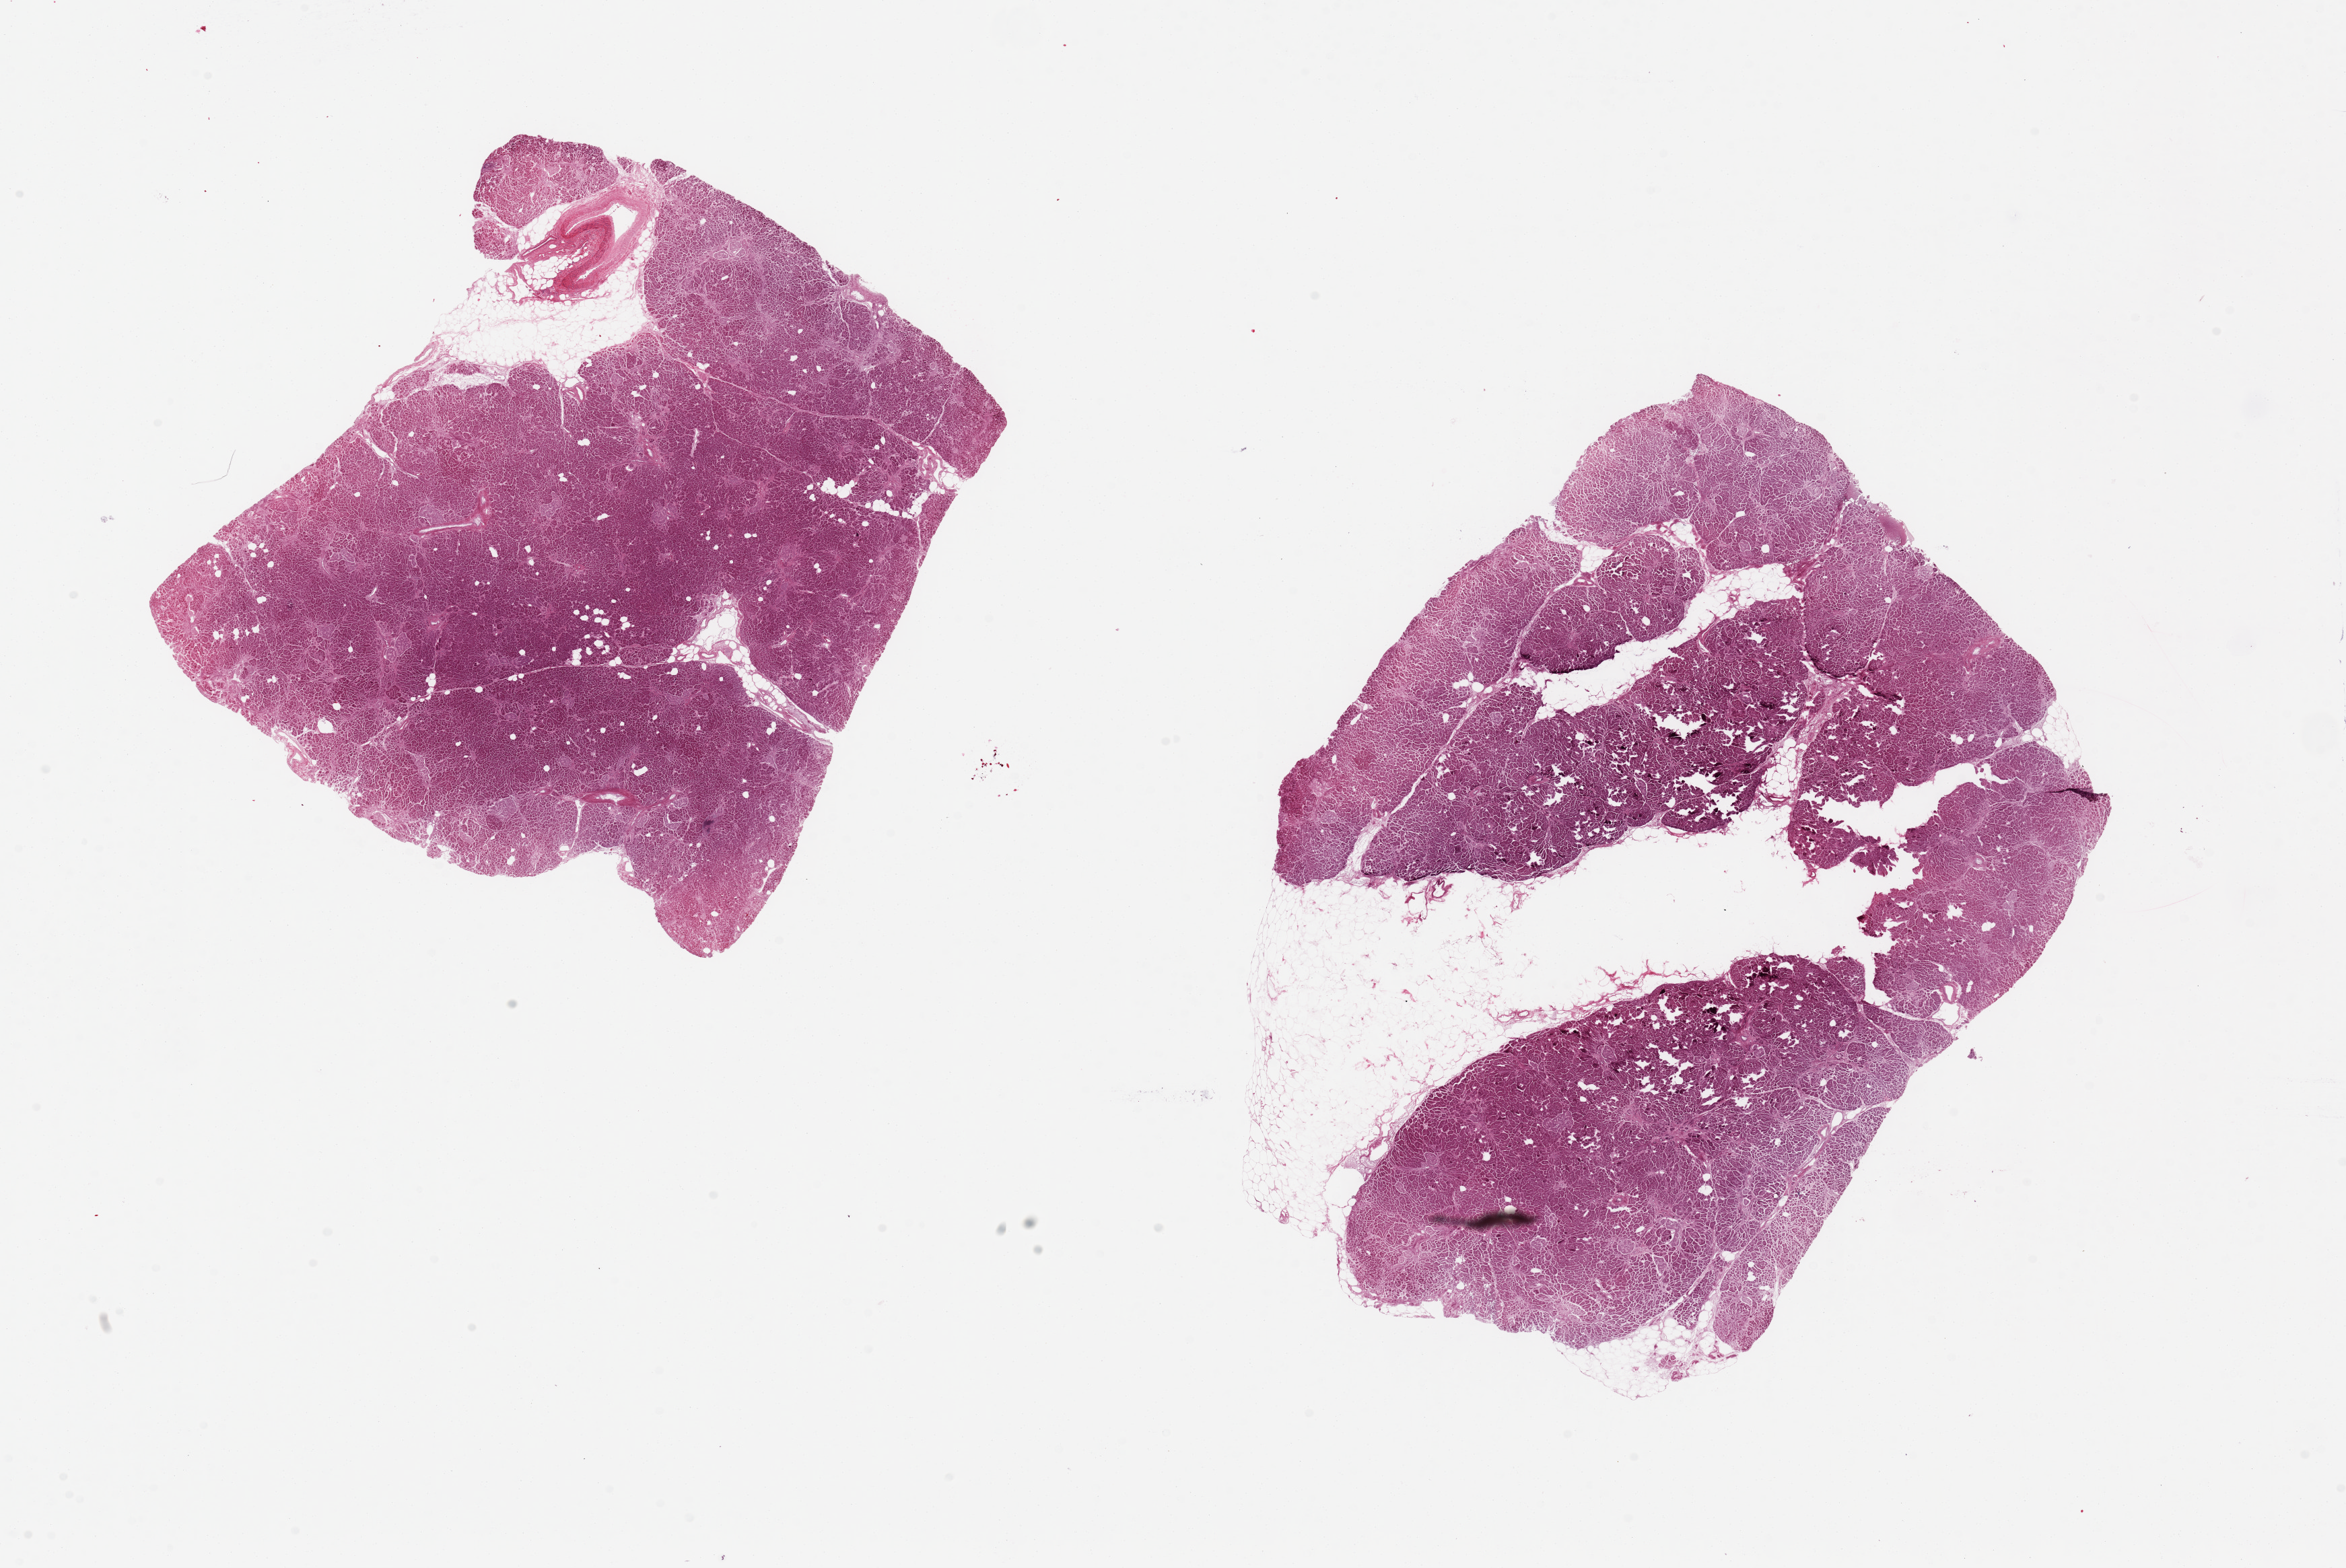
Haematoxylin and eosin whole-slide image, brightfield, shown as a low-resolution overview of the whole scanned area (about 27.6 x 18.4 mm). PAXgene-fixed paraffin-embedded (PFPE) section. Target tissue: pancreas. Tissue donor sample. Donor sex: male.
Reviewer comment on this tissue sample: 2 pieces ~9x8mm; Marked autolysis & saponification; Islets seen; one, all badly autolyzed.